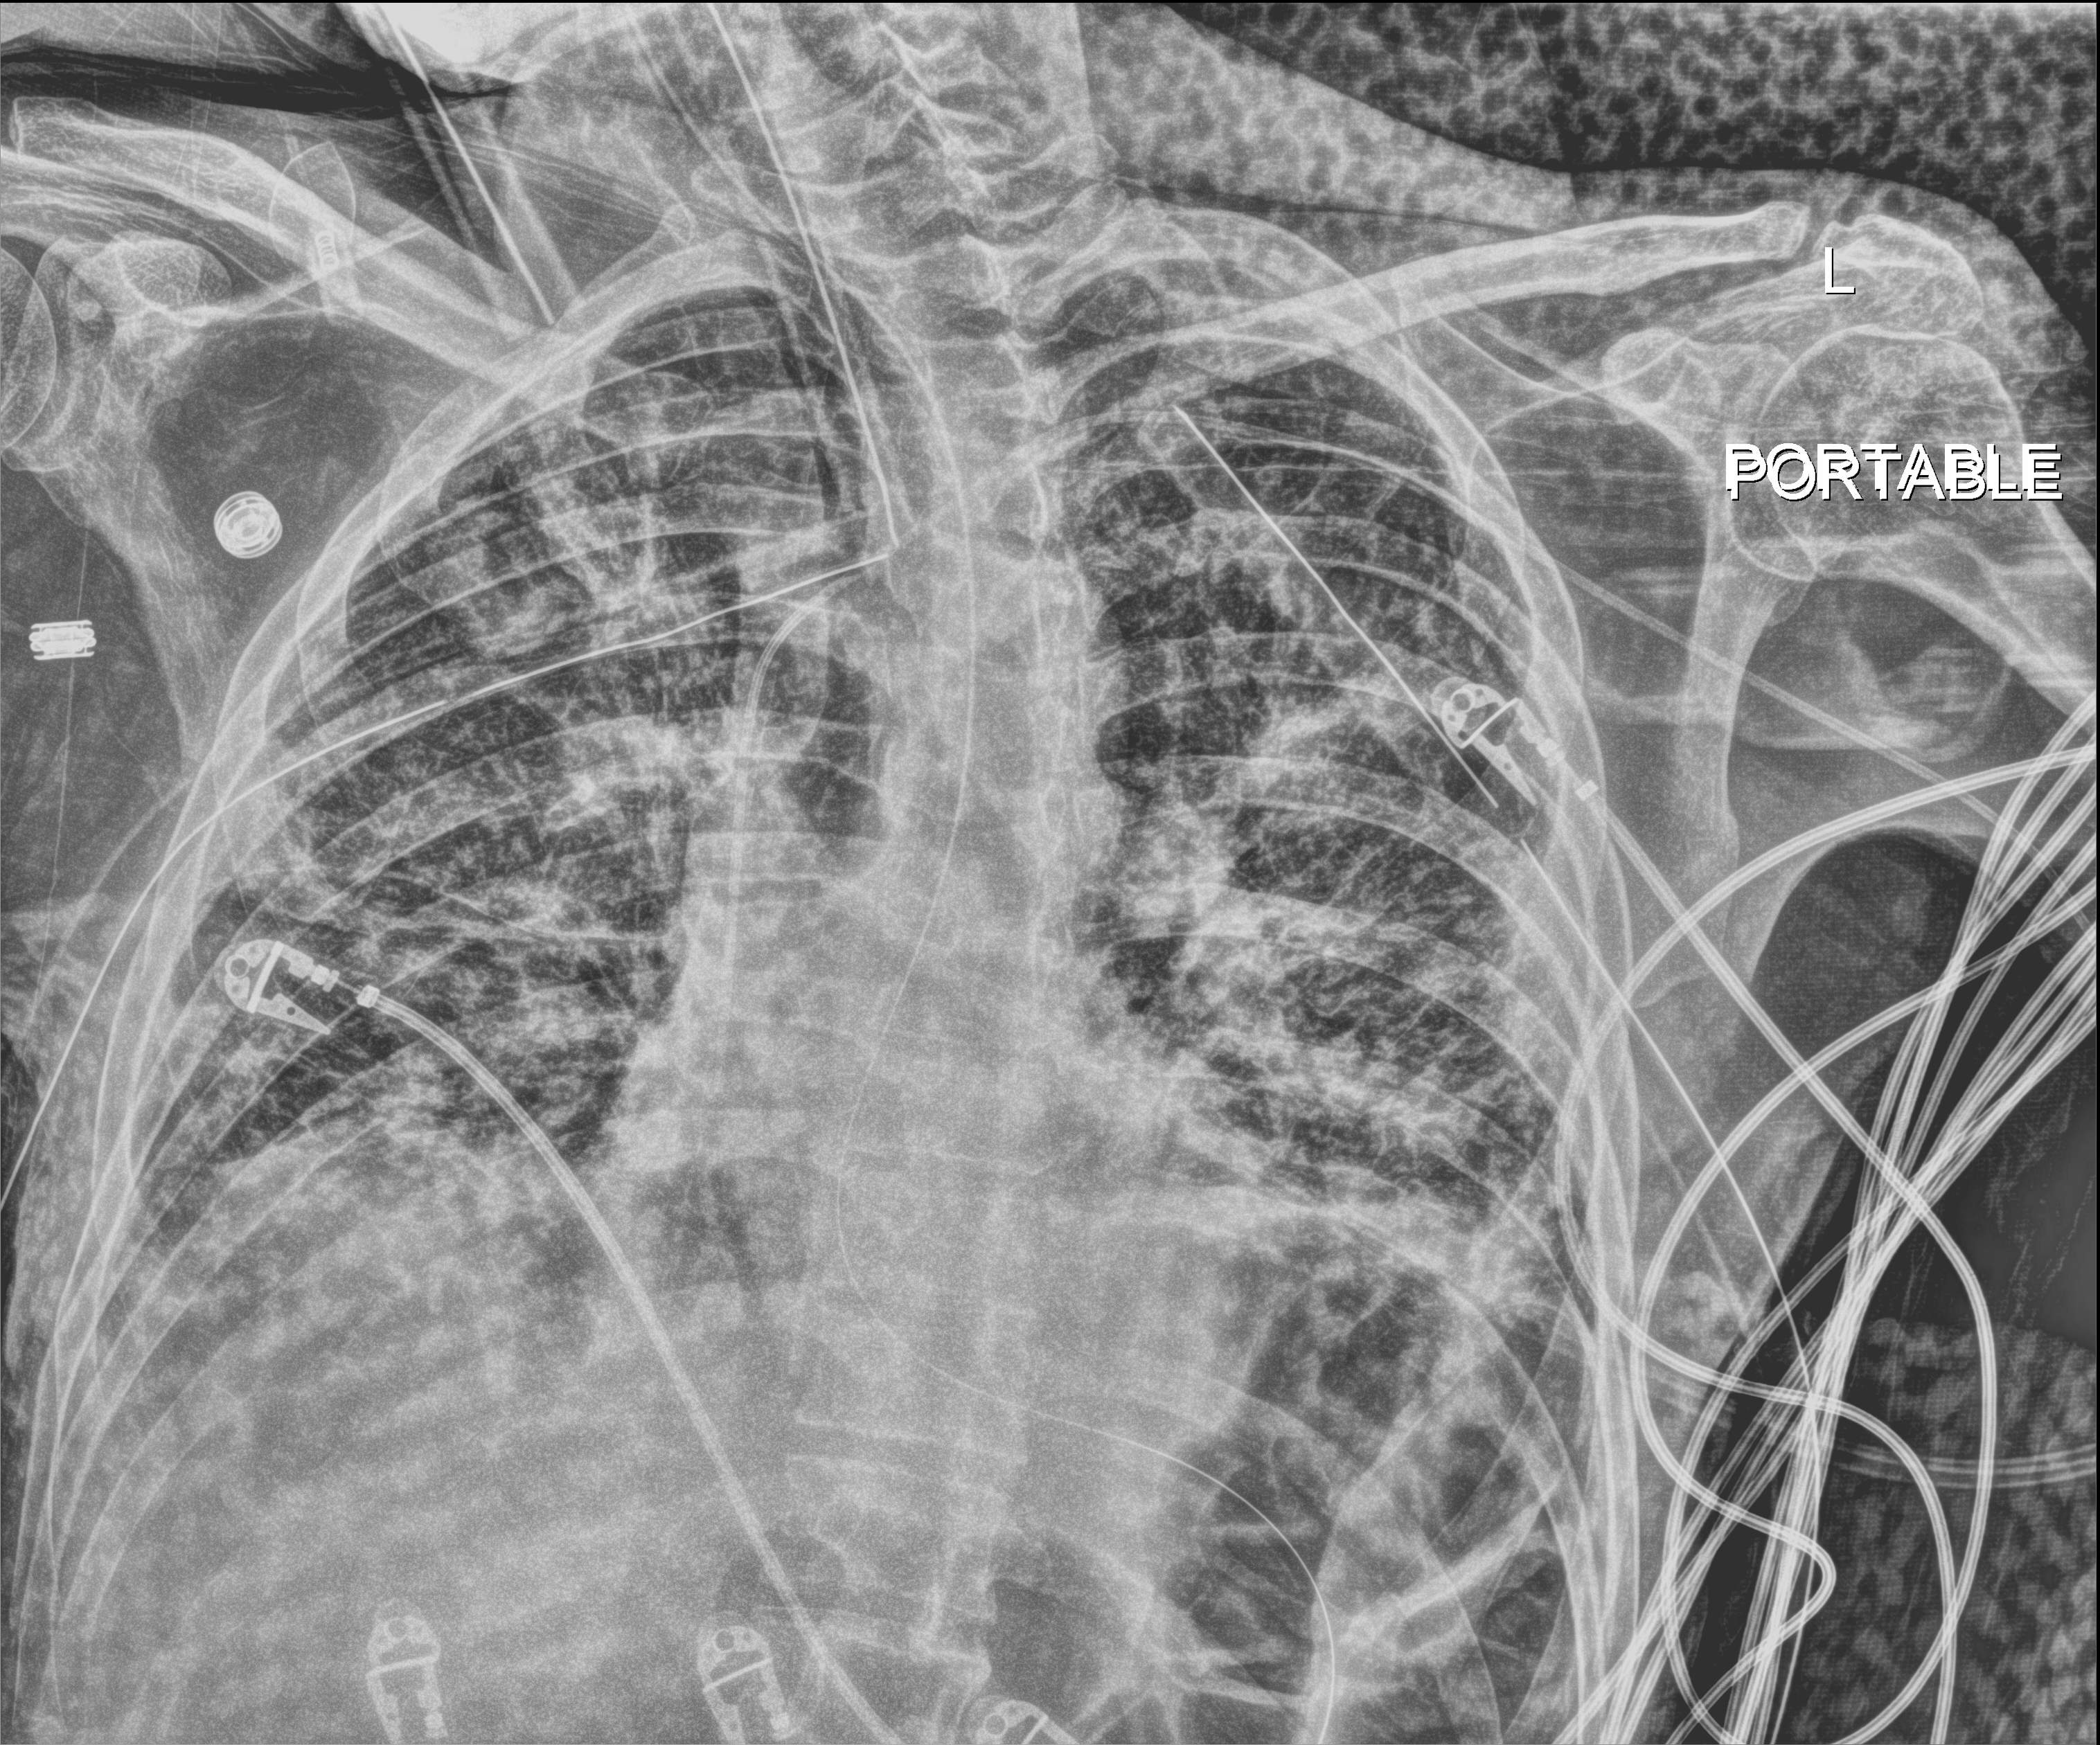
Chest X-ray (portable). Male patient hospitalised with COVID-19, age 18–59 years.
From the hospital-stay record, not from the radiograph (when in the stay this image was taken is not recorded): admitted to intensive care during this hospital stay: yes.